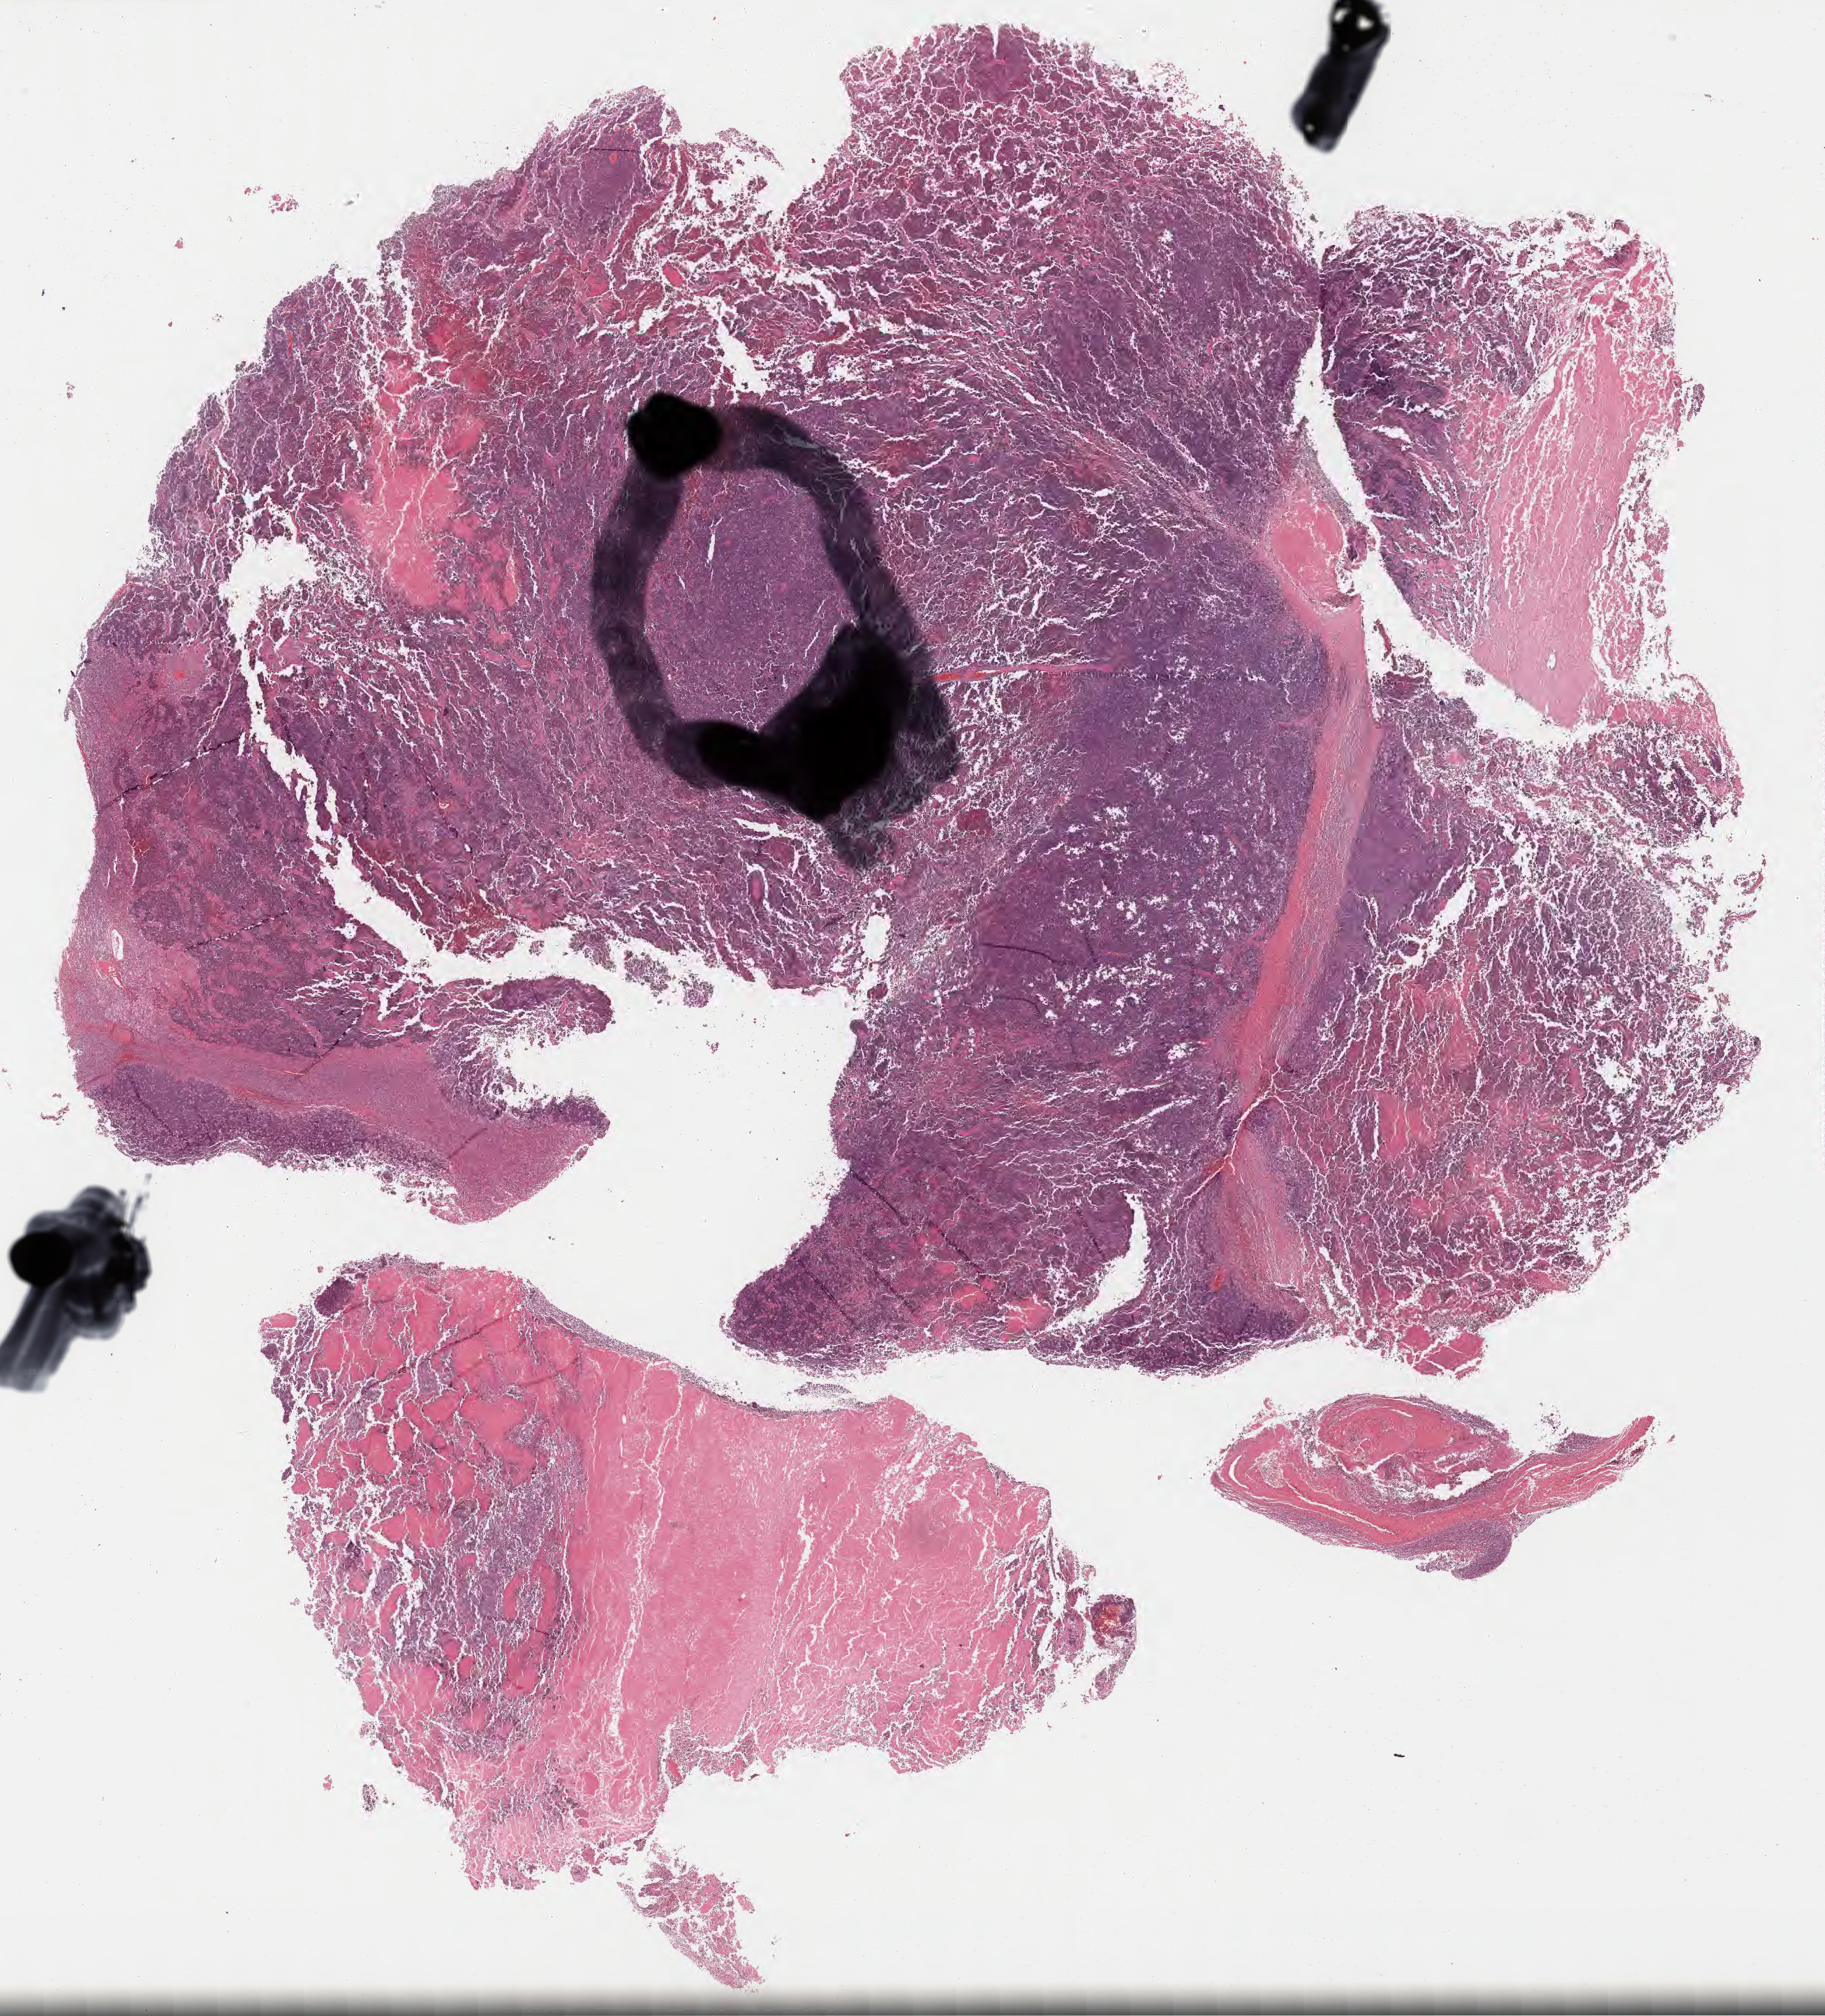
Whole-slide image, H&E stain, low-resolution overview of the scanned area, about 21.1 x 23.3 mm, tumor tissue. Patient female; aged 34.
- diagnosis: Burkitt lymphoma, NOS